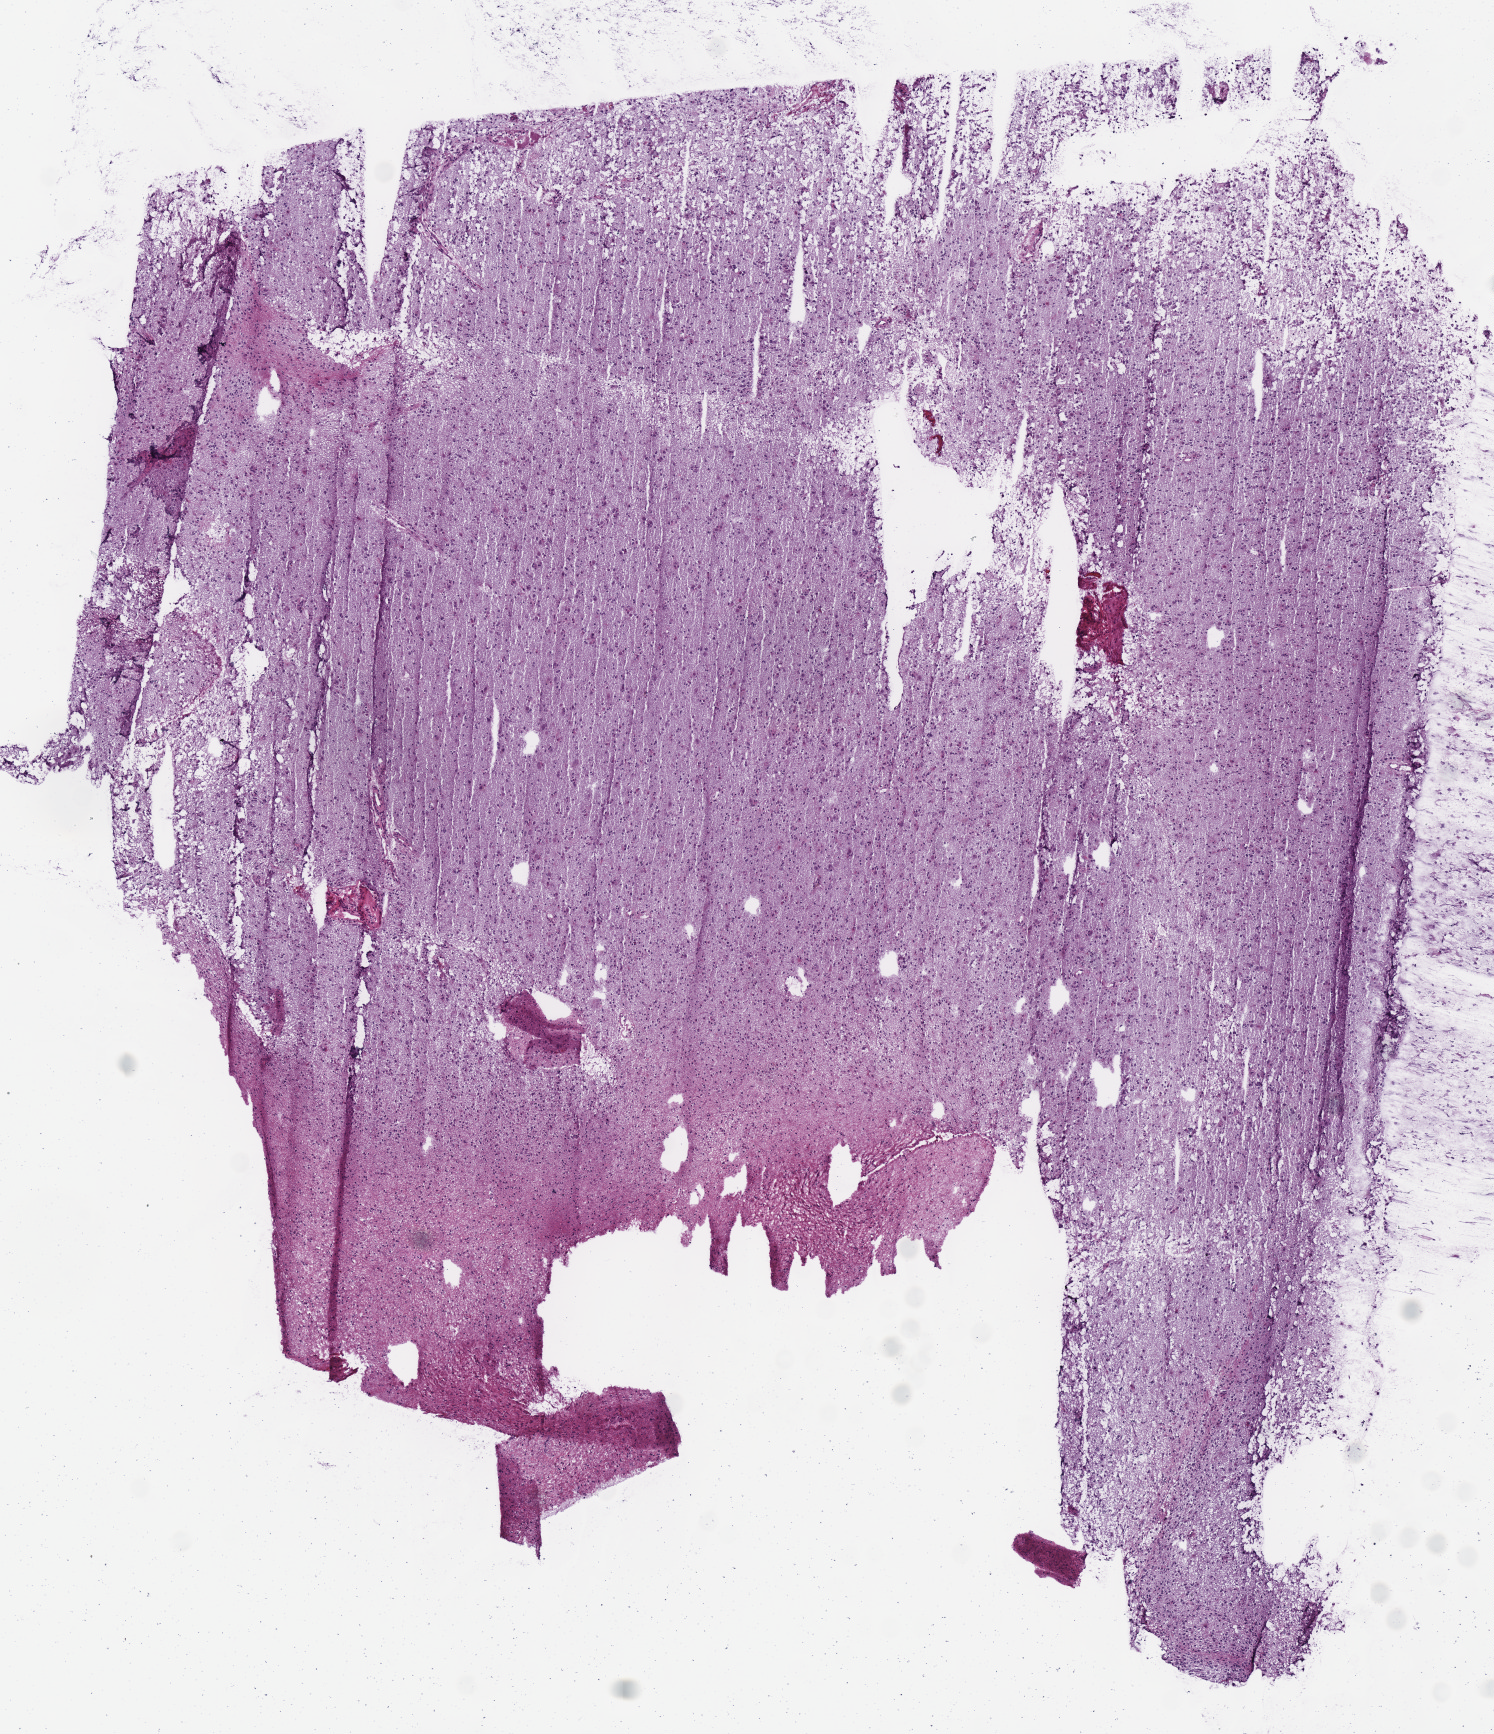
Whole-slide histology image, H&E, whole scanned area (about 5.9 x 6.8 mm, from a 40x scan) shown as a low-resolution overview, frozen section from the top of the tissue portion, brain, primary tumour sample. Patient: male, age at initial diagnosis 62 years. Histologic grade: G3 (poorly differentiated). Slide review estimates, as recorded: tumour cells 100%, tumour nuclei 70%, normal cells 0%, stromal cells 0%, necrosis 0%.
Histologic diagnosis: Mixed glioma (cerebrum). Laterality: left.